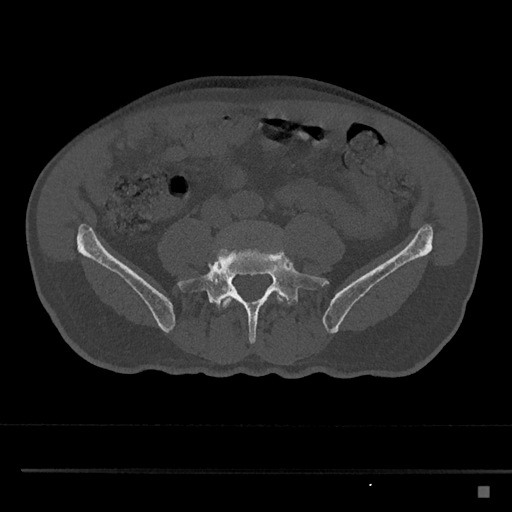
CT including the spine, one axial slice; slice 595 of 797 in the series (ordered by position); reconstruction kernel Br40s/3; 120 kVp; bone window (W 1800 / L 400 HU); 0.5 mm slice thickness; 512 × 512 image matrix, field of view 391 × 391 mm. Patient: male, 59 years. From the clinical record (not read from this slice): primary cancer: prostate.
Outlined on this slice (semi-automatic segmentation, software-assisted and operator-edited):
- L4 vertebra: bounding box (x1, y1, x2, y2) in pixels: (216, 291, 285, 309)
- L5 vertebra: (176, 239, 330, 344)